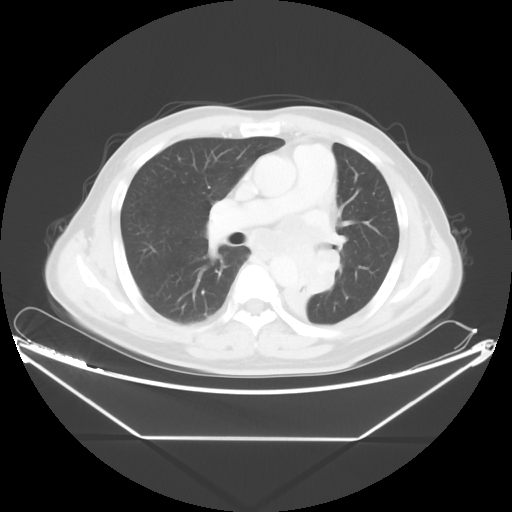
Chest CT, one axial slice; position 26 of 48 along the scan axis; 120 kVp; lung window (W 1500 / L -600 HU); 5 mm slice thickness; 512 × 512 image matrix. Patient: male, 58 years. From the clinical record (not read from this slice): clinical TNM (as recorded): T3 N3 M0.
Annotated regions visible in this slice (rectangle marked by the reading radiologist):
- lung tumour (recorded histology: squamous cell carcinoma): bounding box [x1, y1, x2, y2] px = [286, 245, 340, 326]